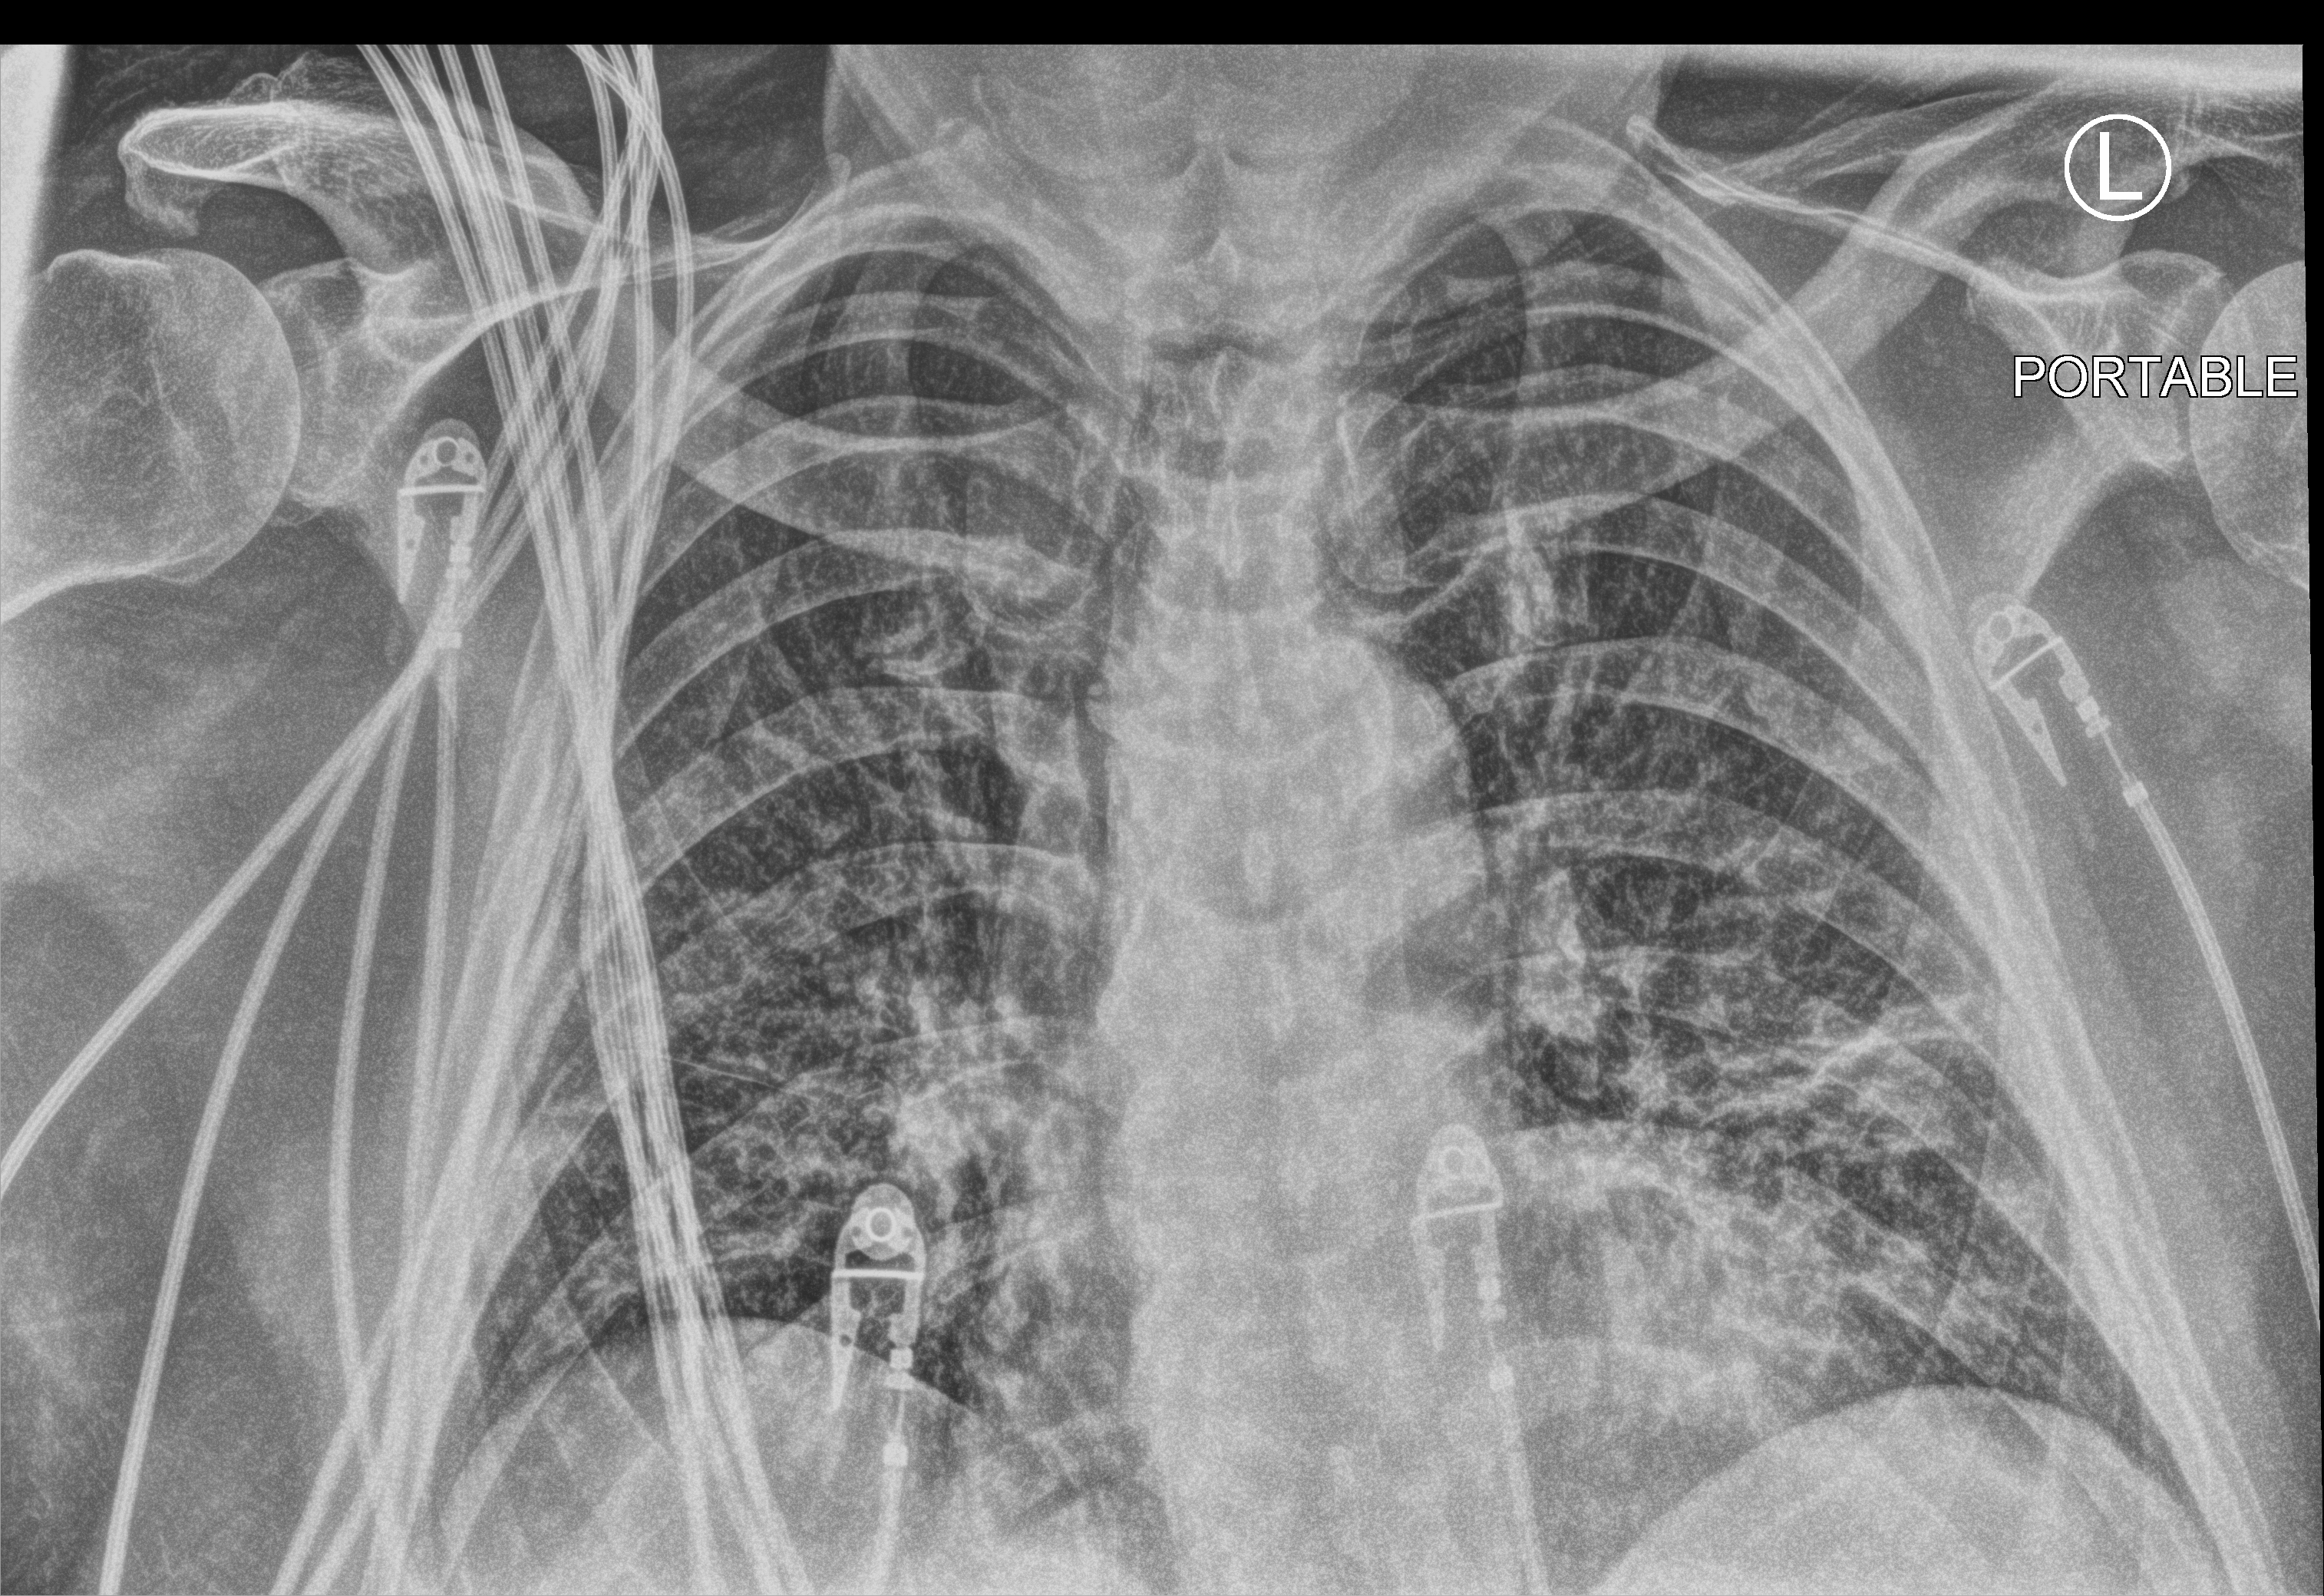
Portable chest radiograph; anteroposterior (AP) projection. Patient hospitalised with COVID-19; male, aged 18–59 years.
Hospital-stay facts (about this admission, not read from this image; timing relative to this image not recorded): mechanically ventilated during this hospital stay: yes; length of hospital stay: 21 days.